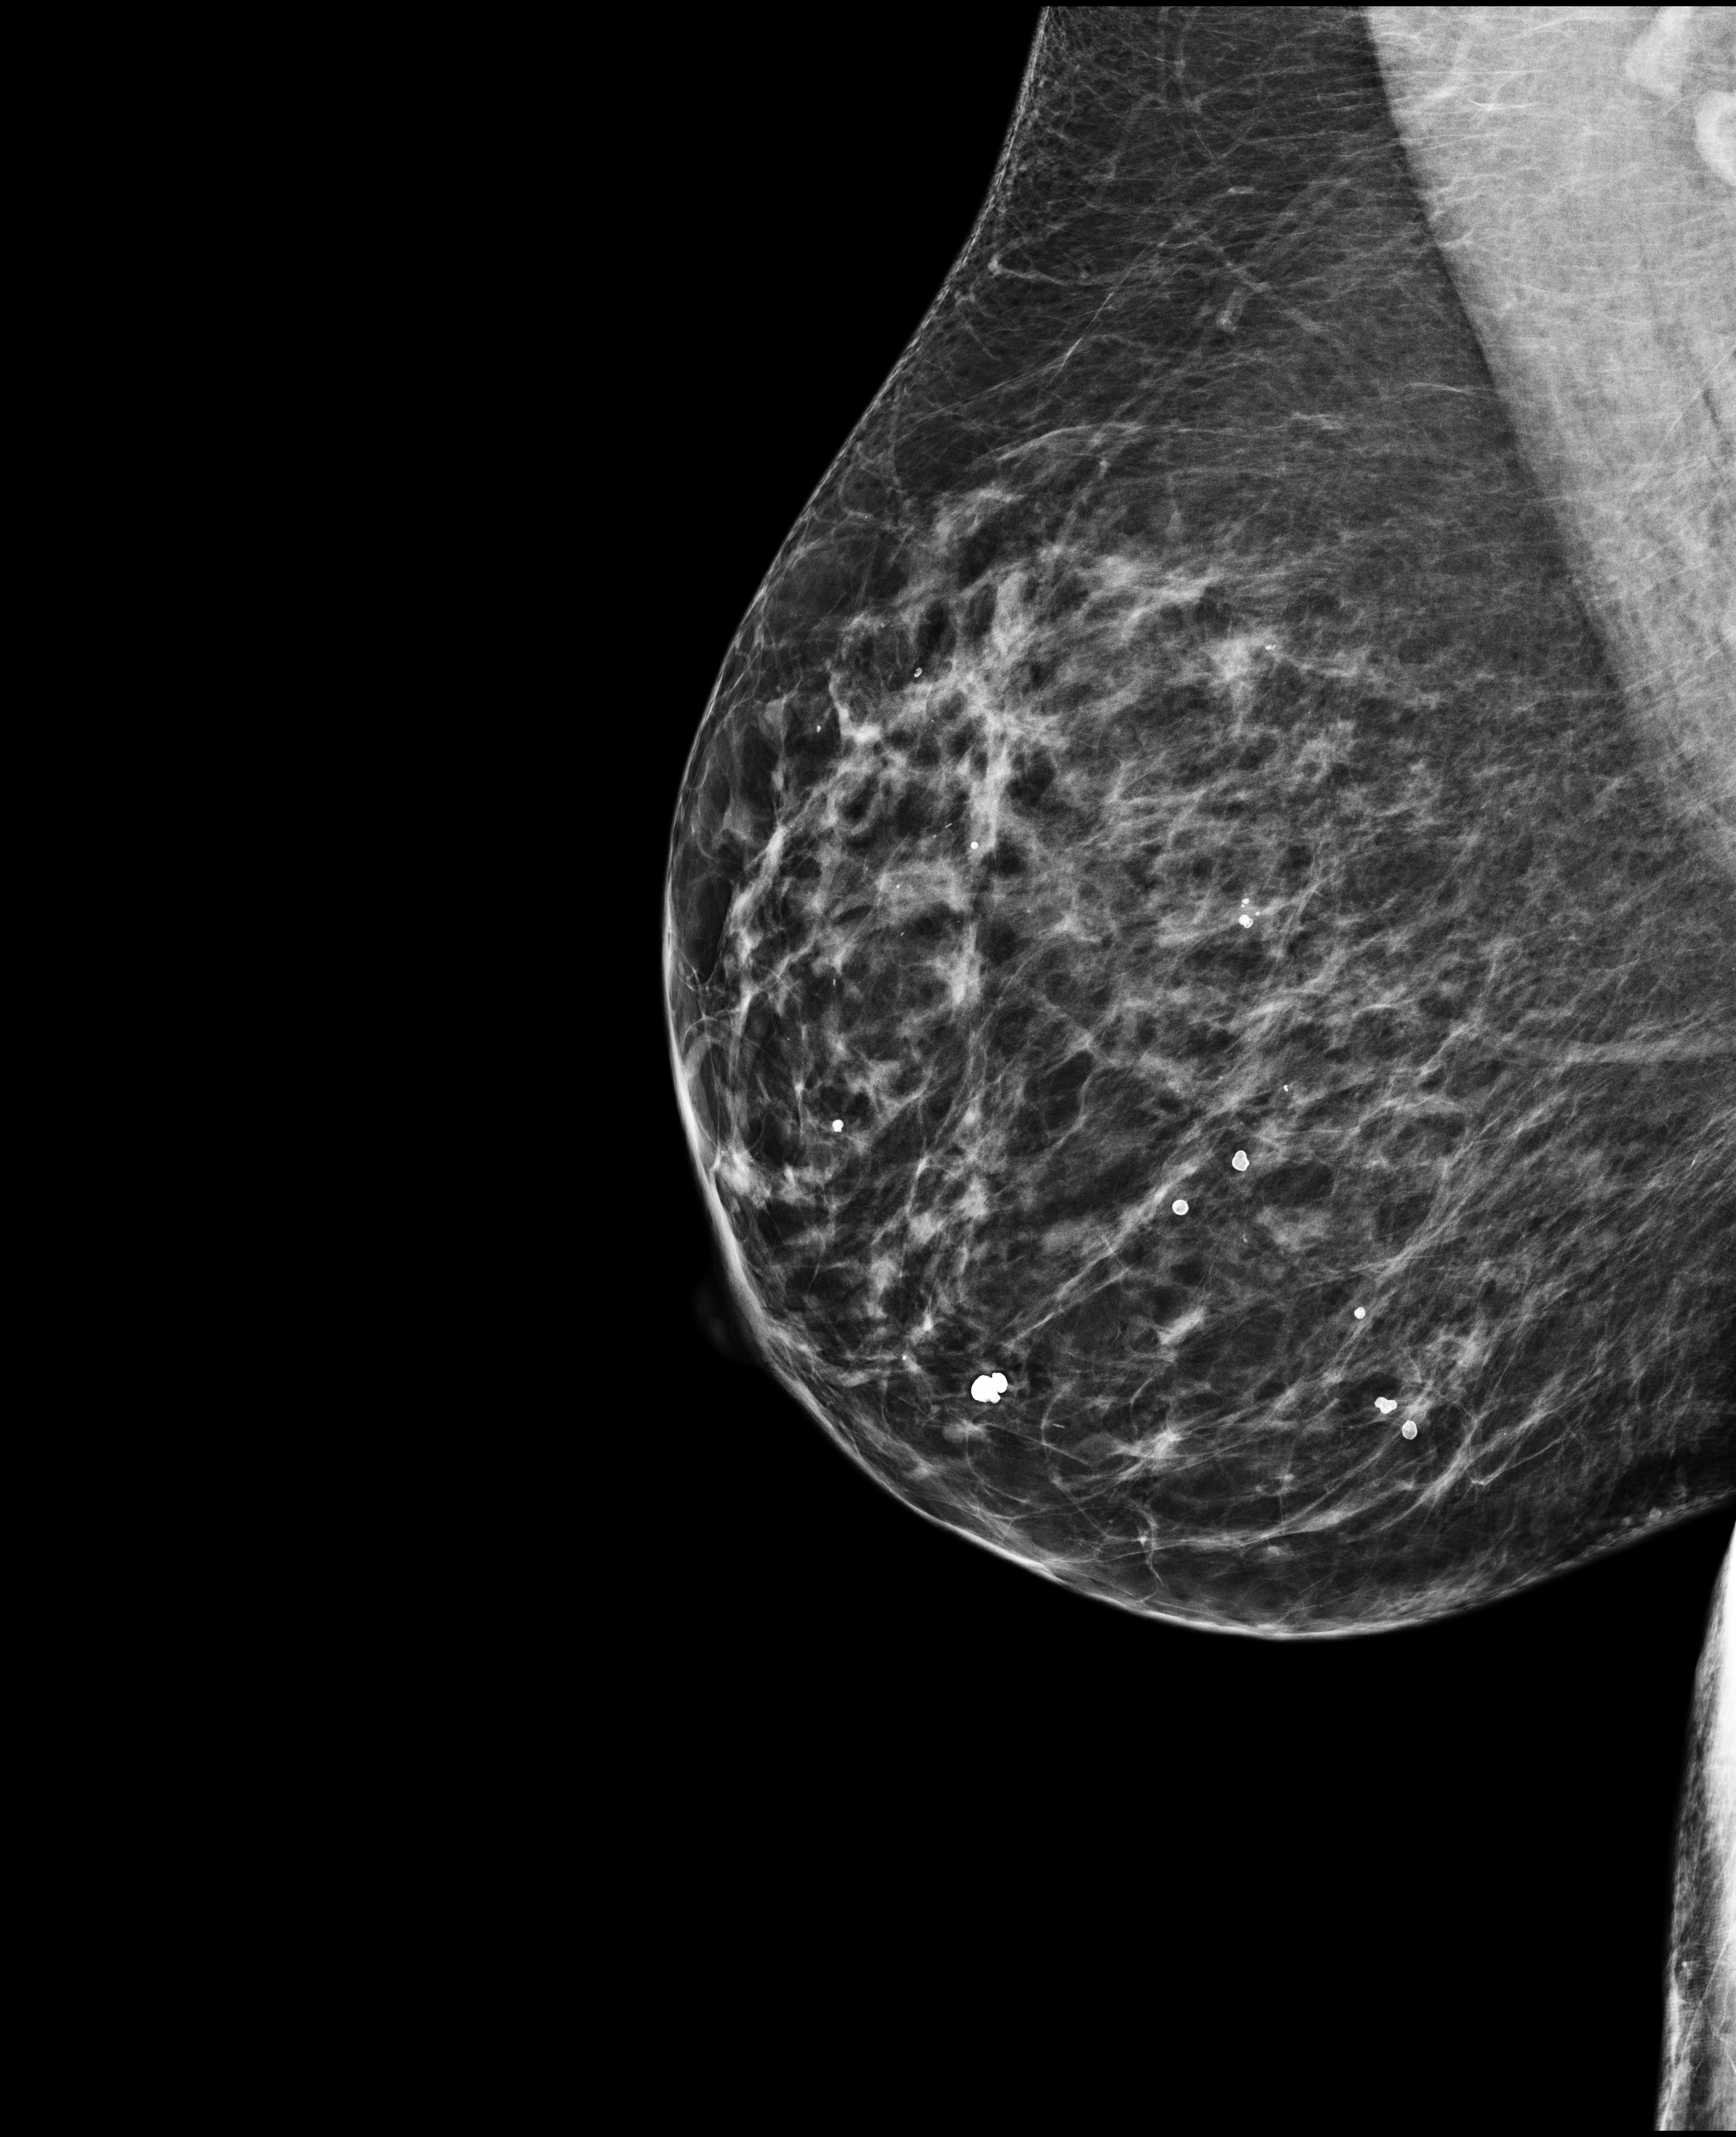
Digital mammogram (FFDM); right breast; MLO view; screening examination; system: Selenia Dimensions. Patient aged 65 years (female).
BI-RADS breast density category at the screening exam (both breasts, scale 1–4): 3. Final BI-RADS category for the screening round (tomosynthesis exam, both breasts): category 2. Recall: no recall after this screen.